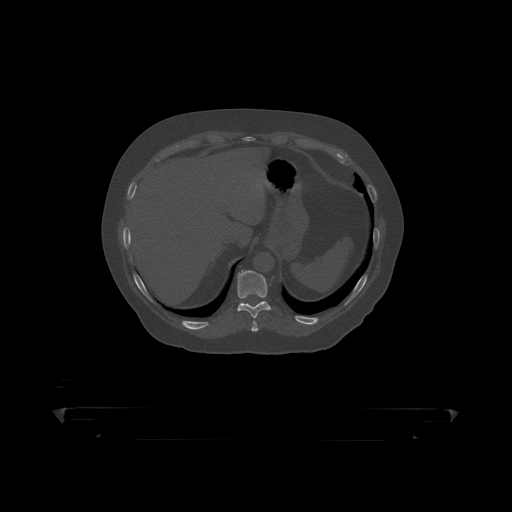
CT including the spine, one axial slice. Position 215 of 390 along the scan axis. Reconstruction kernel STANDARD. 120 kVp. Bone window (W 1800 / L 400 HU). 1.25 mm slice thickness. 512 × 512 image matrix. Patient: male, 60 years. Case-level facts recorded for this patient, not image findings: primary cancer: prostate.
Structures marked on this image (semi-automatically segmented with operator editing):
- T10 vertebra: box from (x=237, y=270) to (x=271, y=319) px